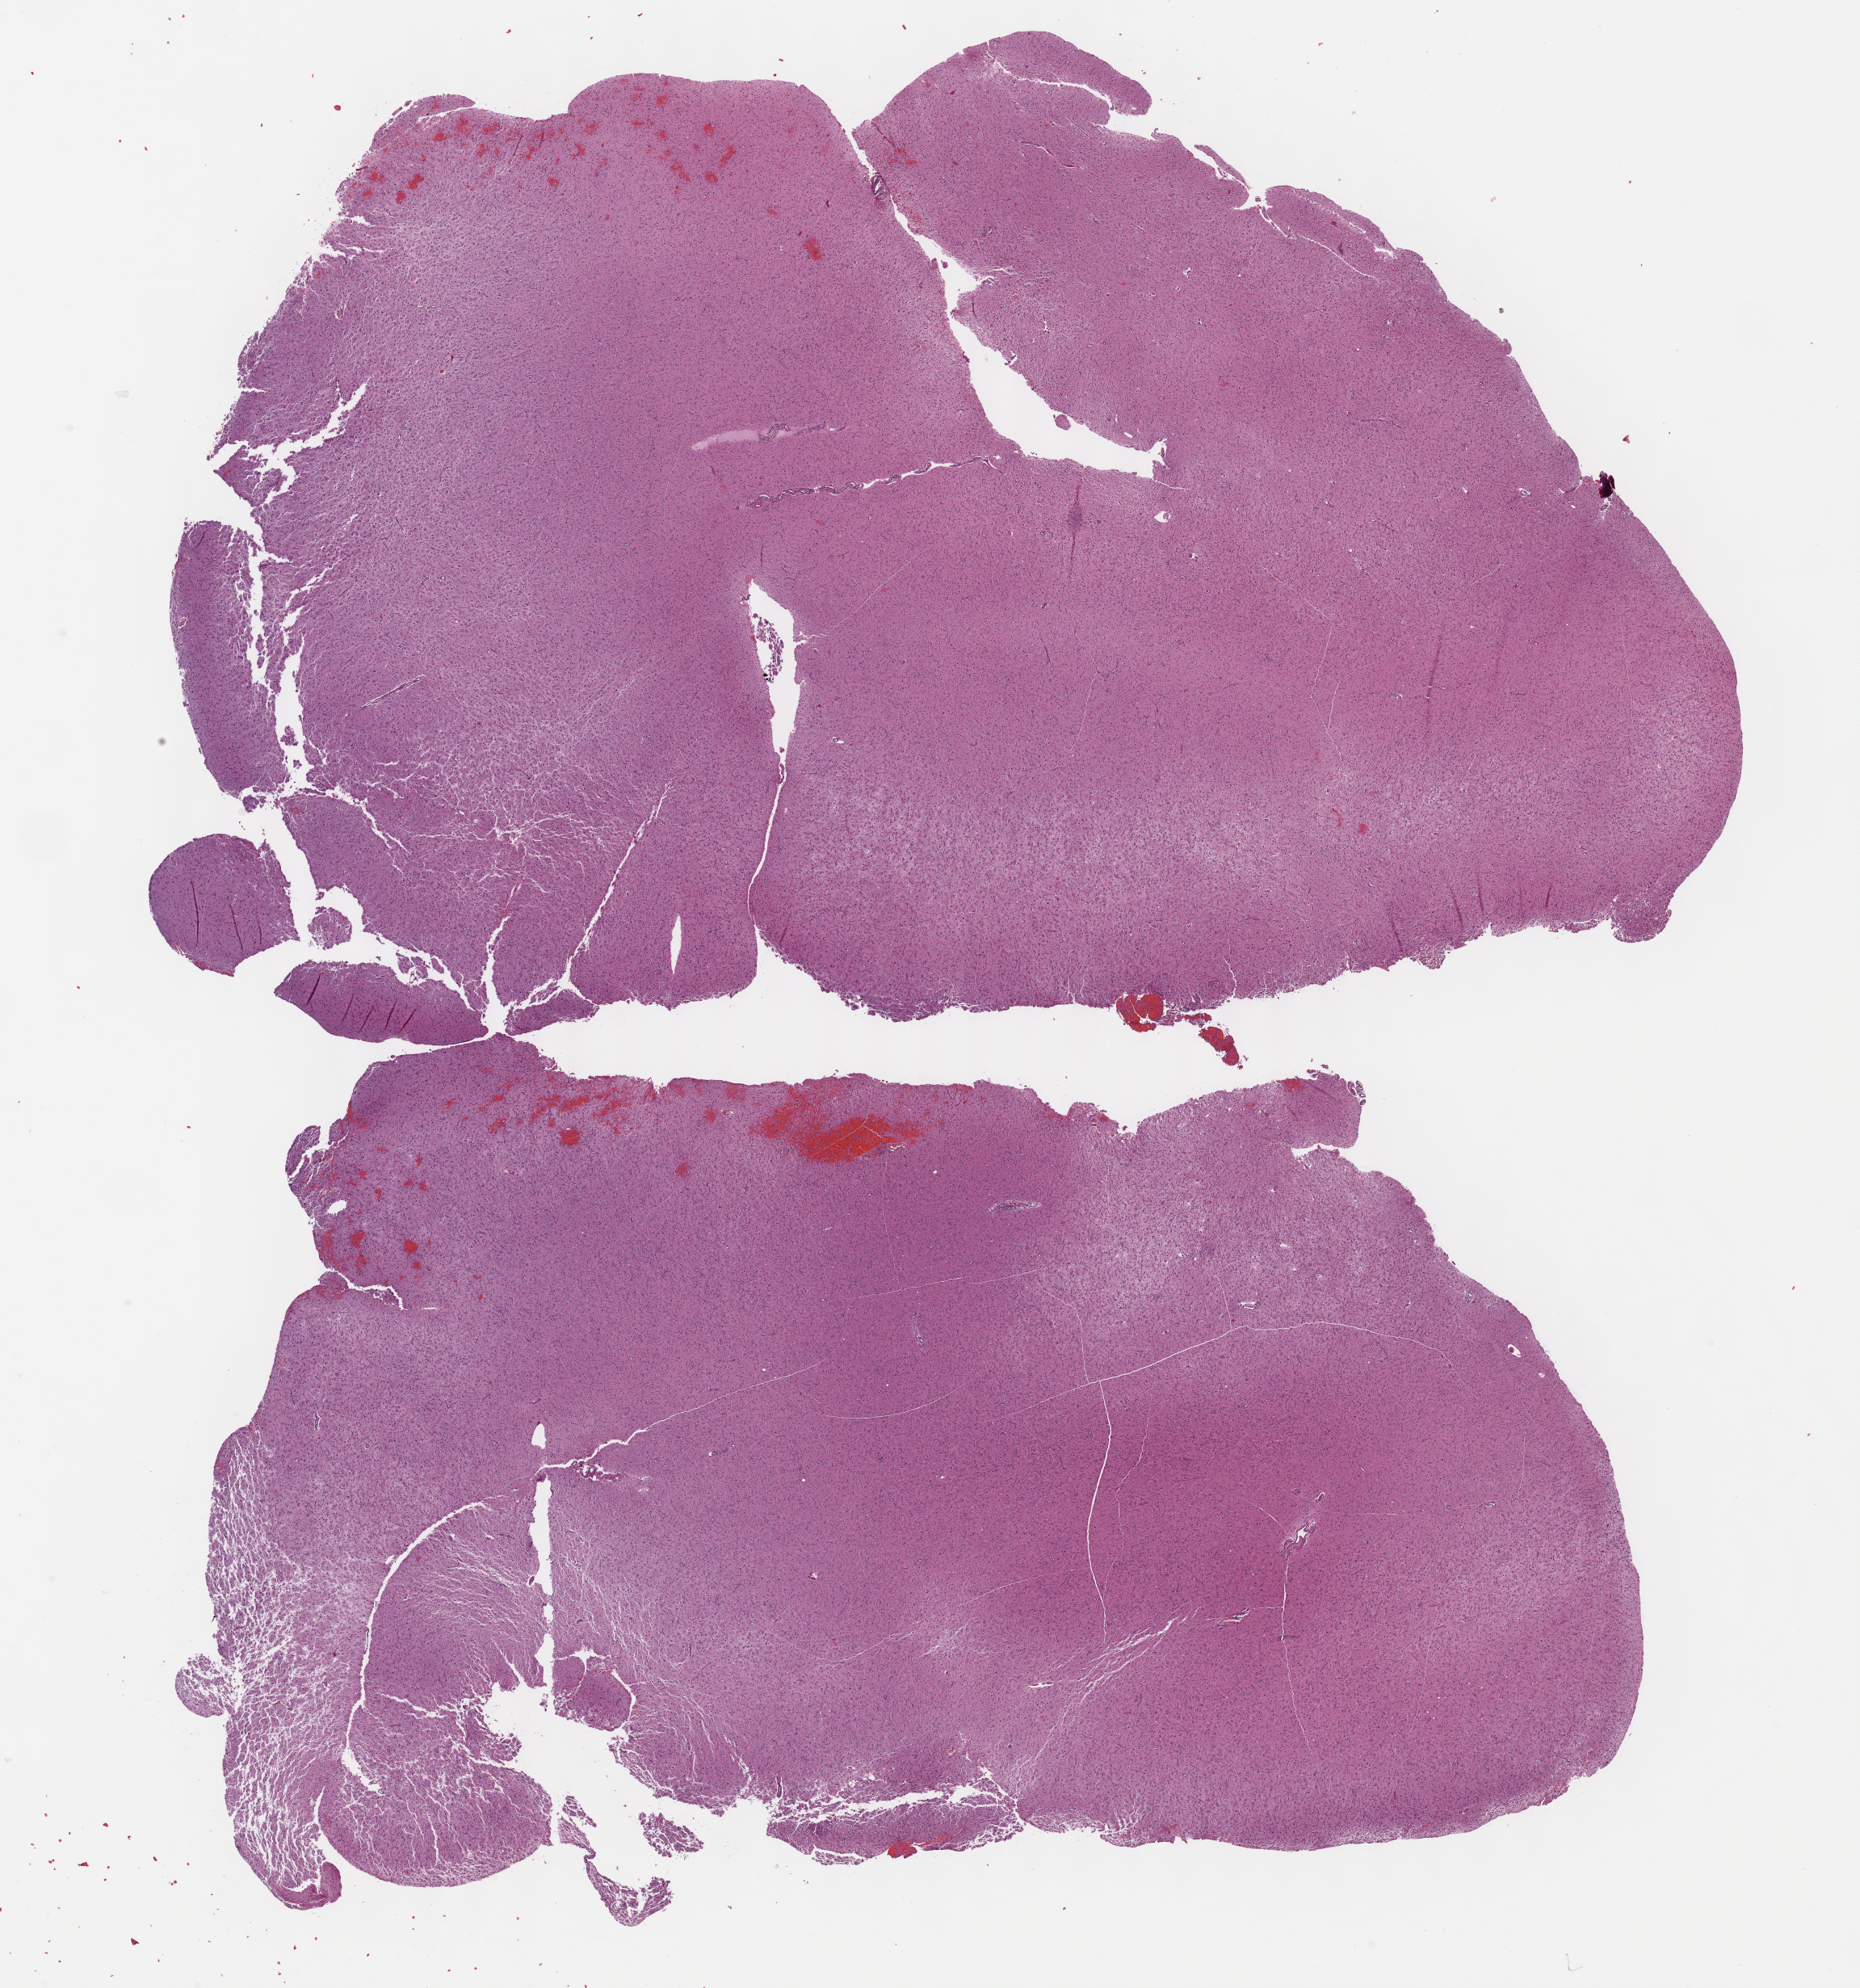
Digitized Hematoxylin and eosin (H&E) stained tissue section (whole slide) — a low-resolution overview of the entire scanned area, about 18.6 x 19.9 mm, formalin-fixed paraffin-embedded (FFPE) diagnostic section, brain, primary tumour sample. Female, age 30 years at initial diagnosis. Histologic grade: G3 (poorly differentiated).
• laterality: left
• pathologic diagnosis: Astrocytoma, anaplastic